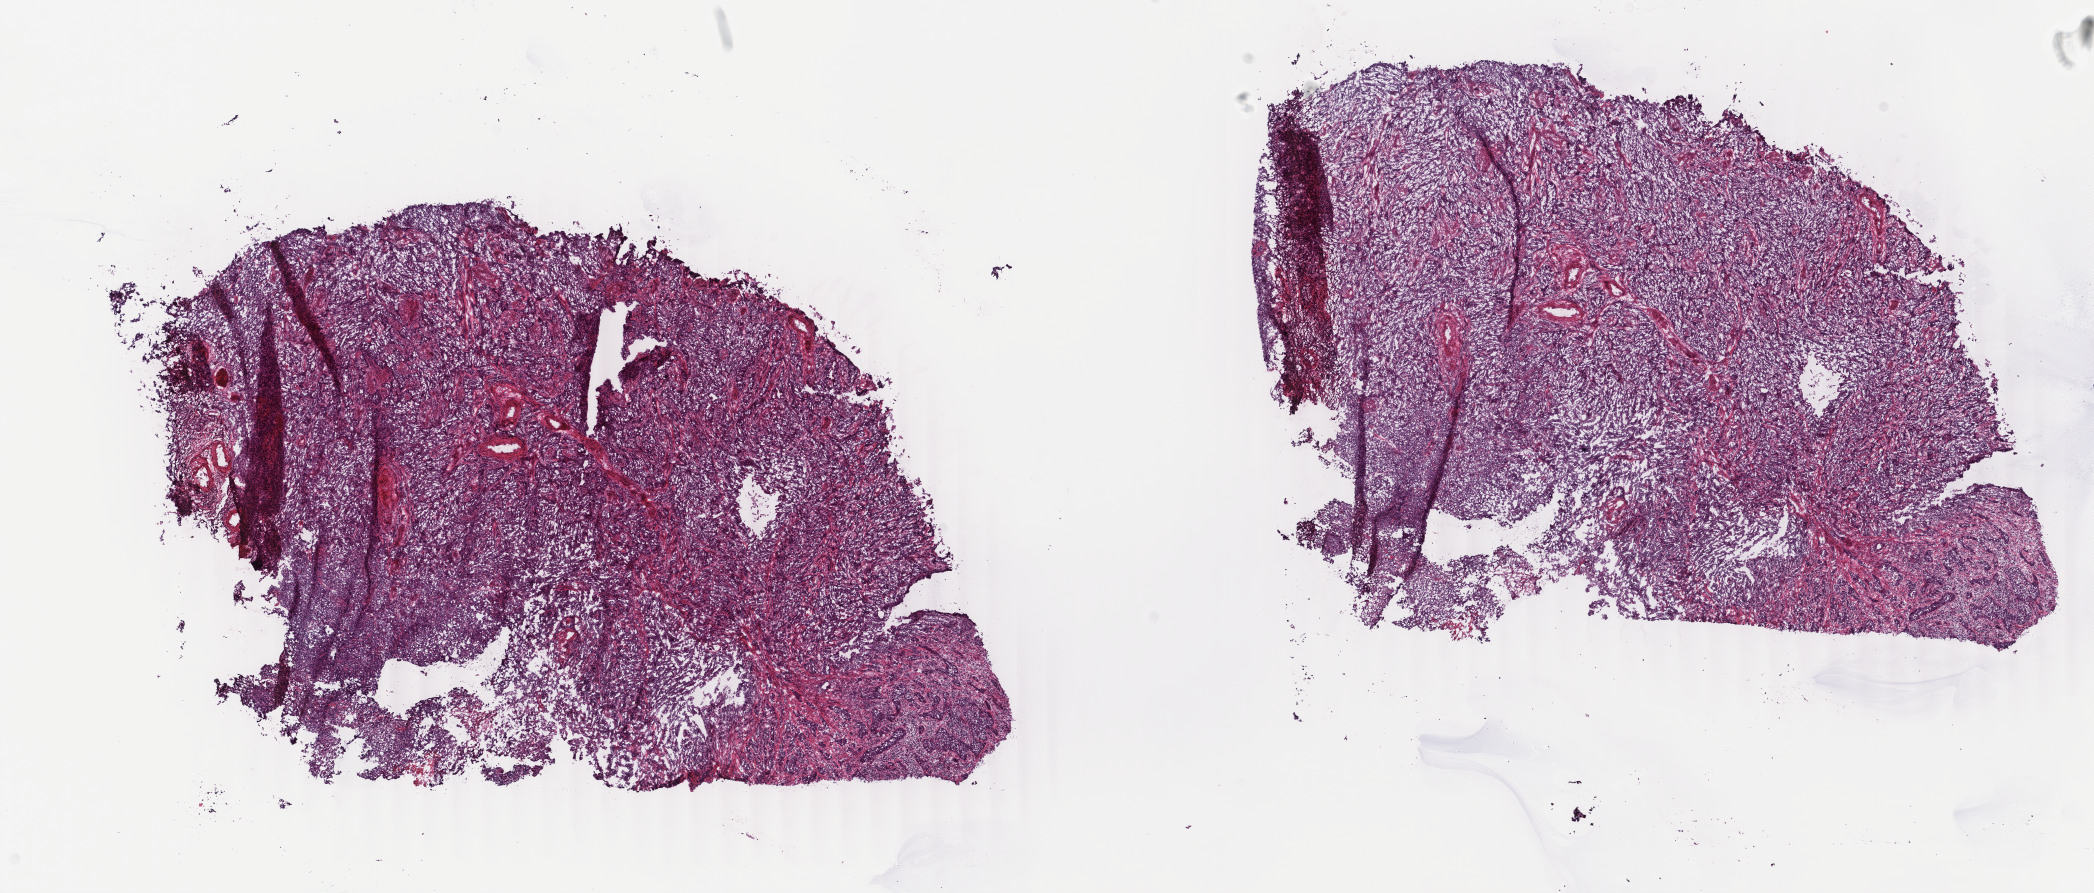
Whole-slide histology image, Hematoxylin and eosin (H&E) stained — low-resolution overview of the scanned area, about 16.7 x 7.1 mm (acquisition: 40x scan), frozen section, sample: primary tumour, cervix. Female, age 49 years at initial diagnosis. Histologic grade: G3 (poorly differentiated). Slide review estimates, as recorded: tumour cells 80%, tumour nuclei 80%, normal cells 0%, stromal cells 15%, necrosis 5%. Inflammatory infiltration, as recorded: lymphocyte infiltration 40%, monocyte infiltration 5%, neutrophil infiltration 30%.
* FIGO stage: IB1
* lymph nodes positive (case pathology): 0 of 16 examined
* diagnosis: Squamous cell carcinoma, NOS (cervix uteri)